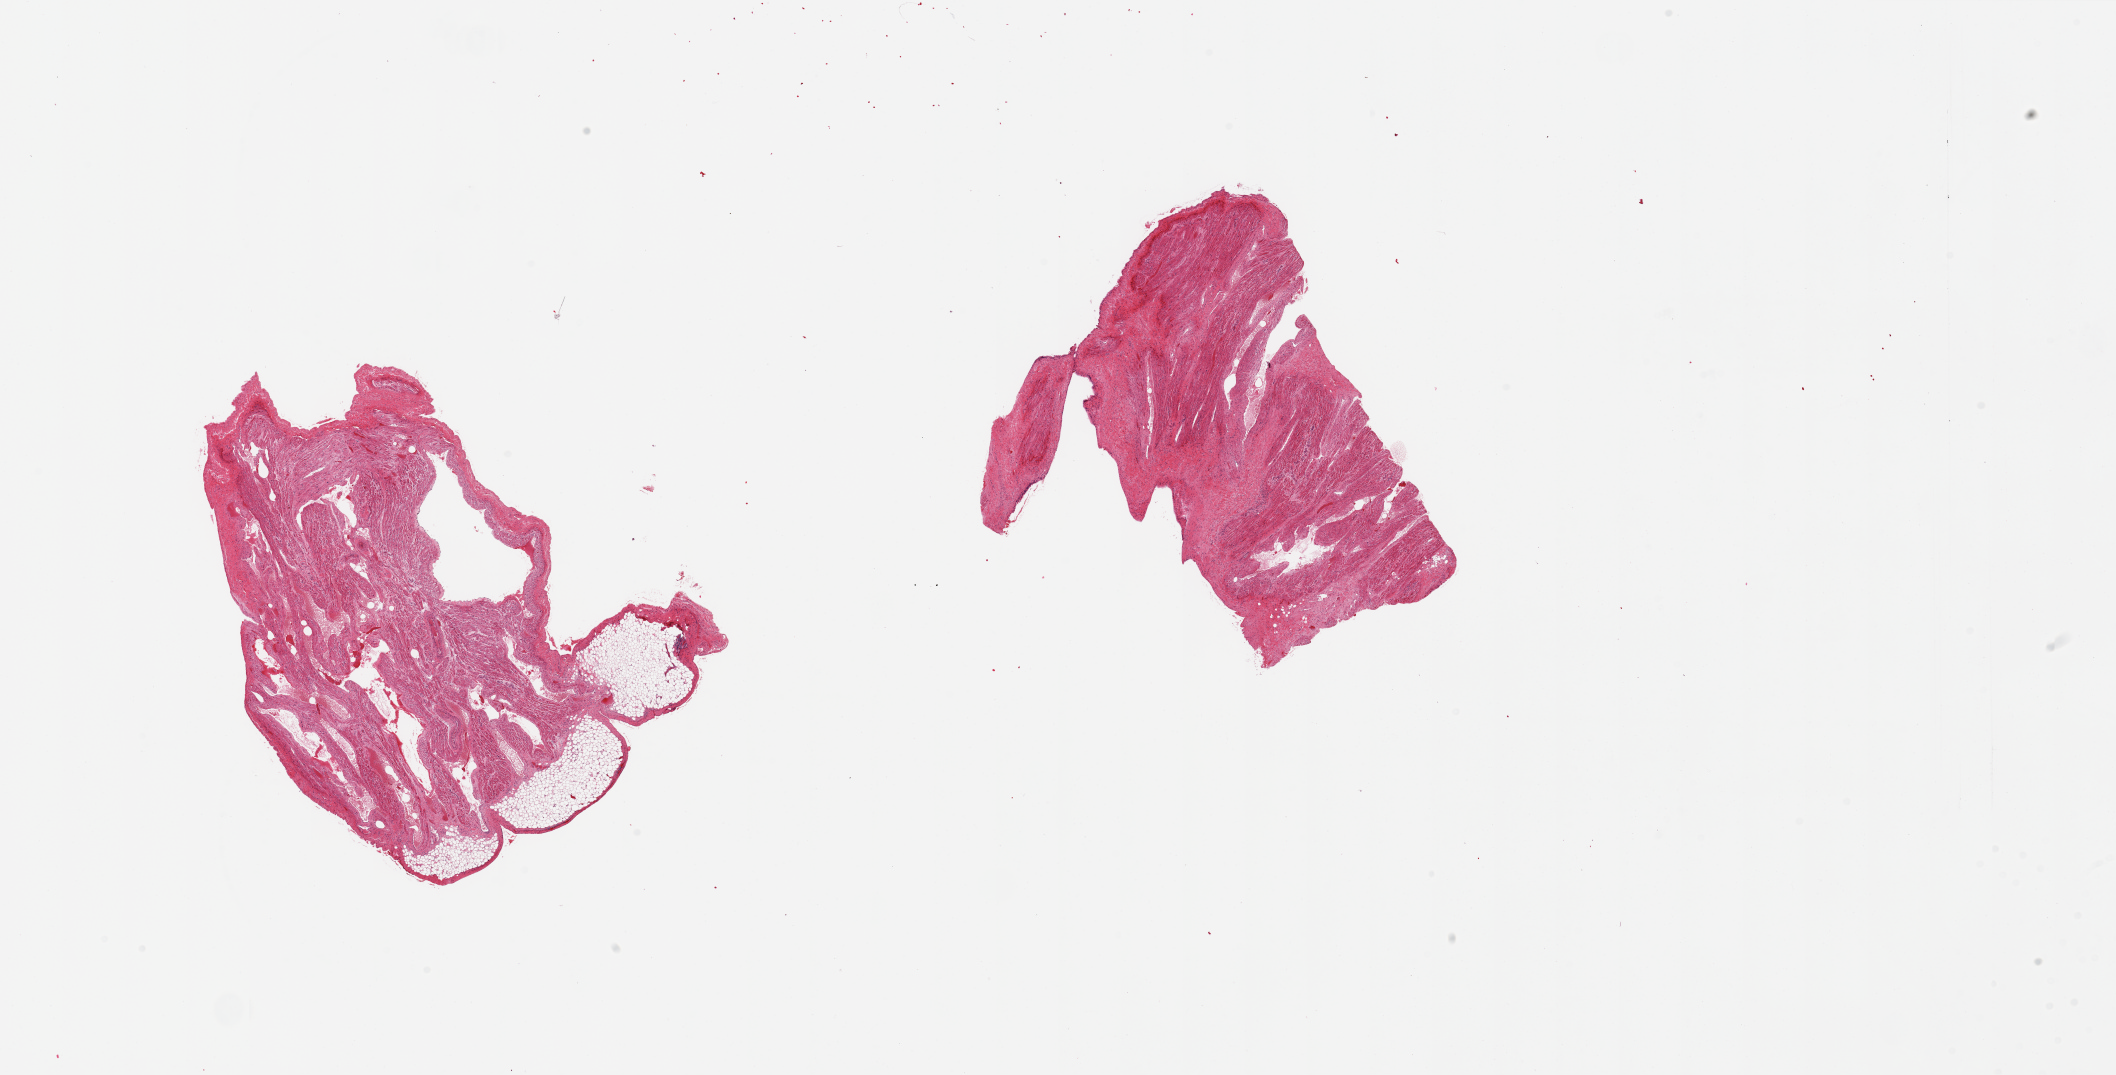
Digitized hematoxylin and eosin (H&E)-stained section, brightfield, low-resolution overview of the scanned area, about 33.5 x 17.0 mm. PAXgene-fixed paraffin-embedded (PFPE) section. Sampled site (target tissue): auricular appendage. Tissue donor sample. Male donor.
* pathologist's review note for this sample: 2 pieces trace adherent fat